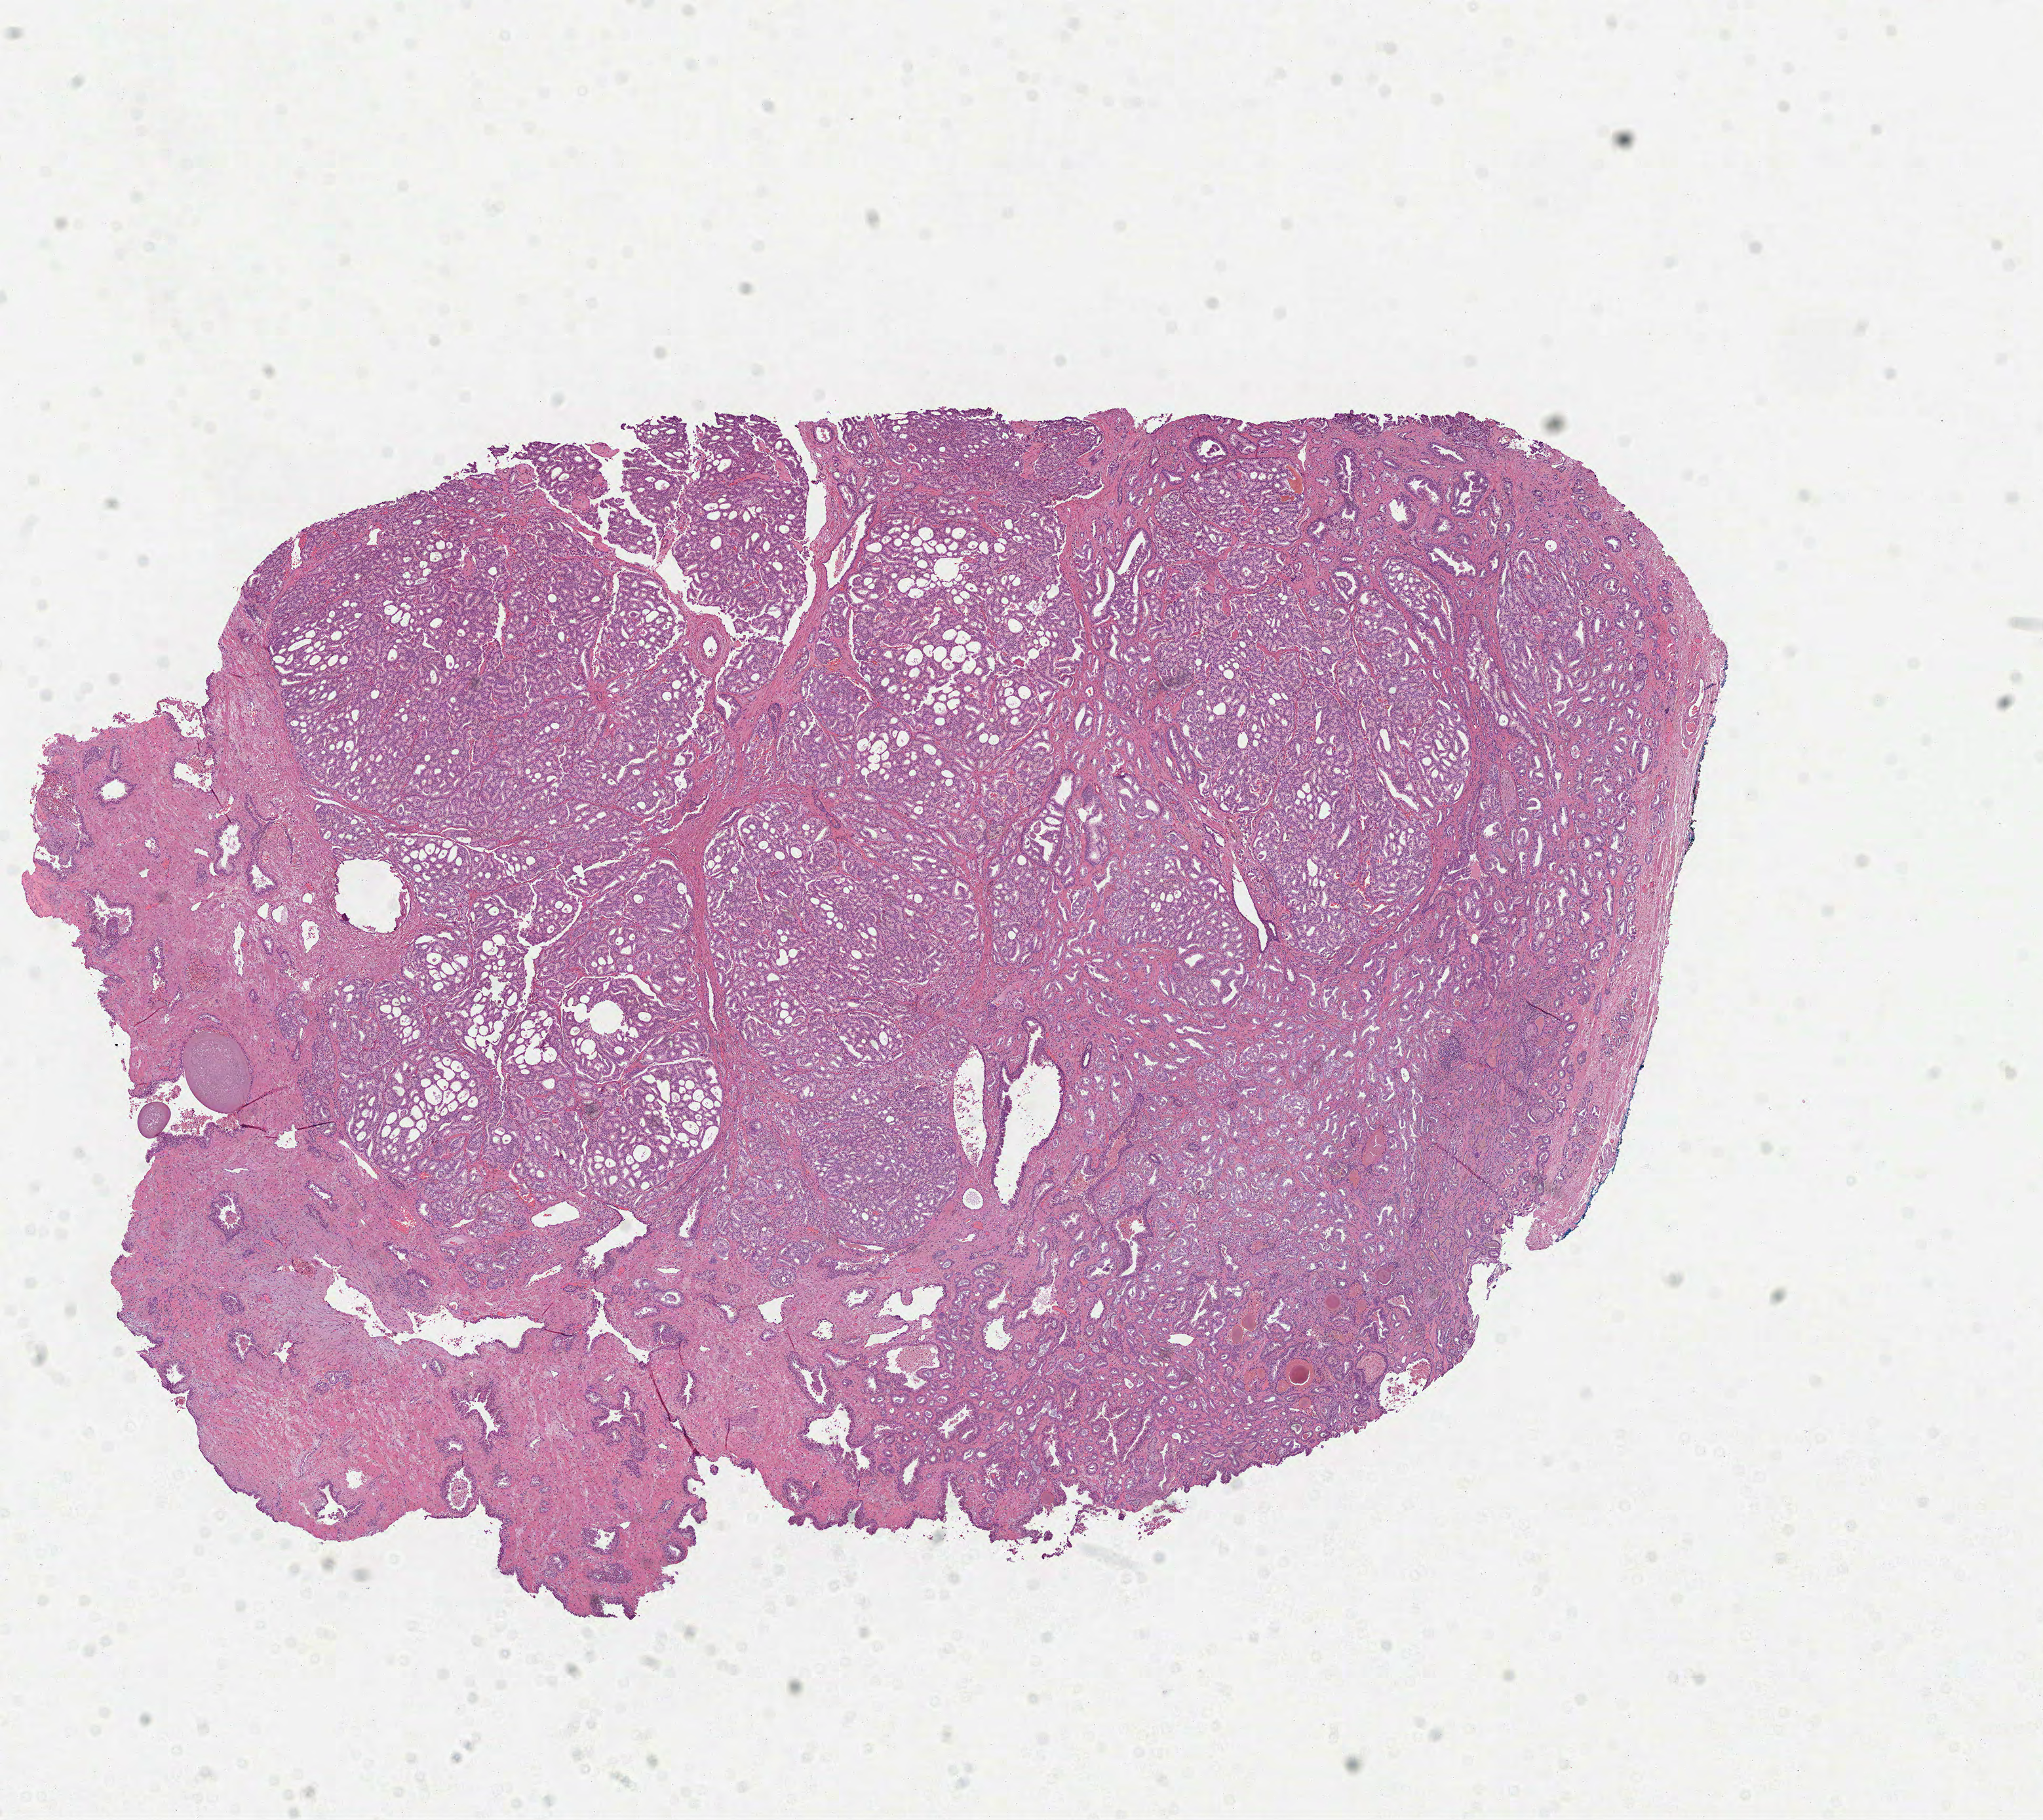
H&E-stained whole-slide image — shown as a low-resolution overview of the whole scanned area (about 12.6 x 11.2 mm), formalin-fixed paraffin-embedded (FFPE) diagnostic section, sample: primary tumour, prostate. Patient: male, age at initial diagnosis 62 years.
Histologic diagnosis: Acinar cell carcinoma (prostate gland).